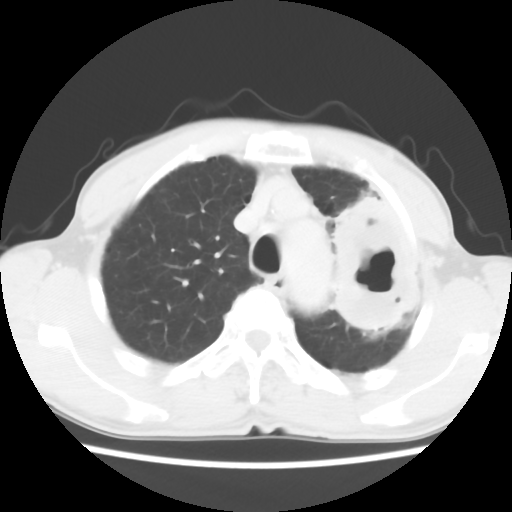
Chest CT, one axial slice. Position 46 of 60 along the scan axis. Reconstruction kernel STANDARD. Lung window (W 1500 / L -600 HU). 5 mm slice thickness. 512 × 512 image matrix, field of view 308 × 308 mm. Male patient, age 64 years. Case-level facts recorded for this patient, not image findings: clinical TNM (as recorded): T3 N3 M0; histopathological grade: G3.
Outlined on this slice (rectangle marked by the reading radiologist):
- lung tumour (recorded histology: adenocarcinoma): bounding box [x1, y1, x2, y2] px = [310, 185, 430, 338]